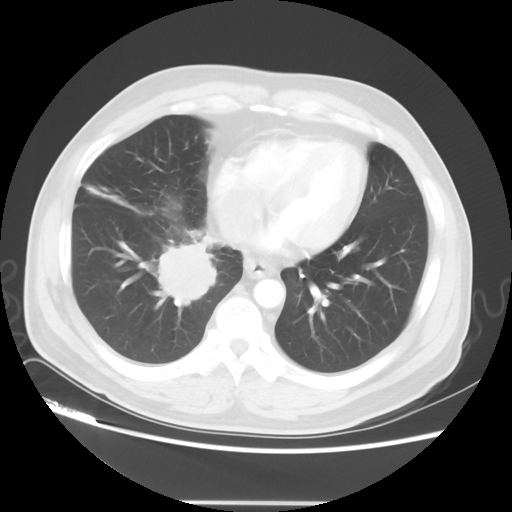
Chest CT, one axial slice. Position 15 of 48 along the scan axis. 120 kVp. Lung window (W 1500 / L -600 HU). 5 mm slice thickness. 512 × 512 image matrix, field of view 390 × 390 mm. Patient: male, 53 years. From the clinical record (not read from this slice): clinical TNM (as recorded): T2 N3 M0; histopathological grade: G3.
Annotated regions visible in this slice (rectangle marked by the reading radiologist):
- lung tumour (recorded histology: small cell carcinoma): bounding box <140,232,228,315> (left, top, right, bottom; pixels)